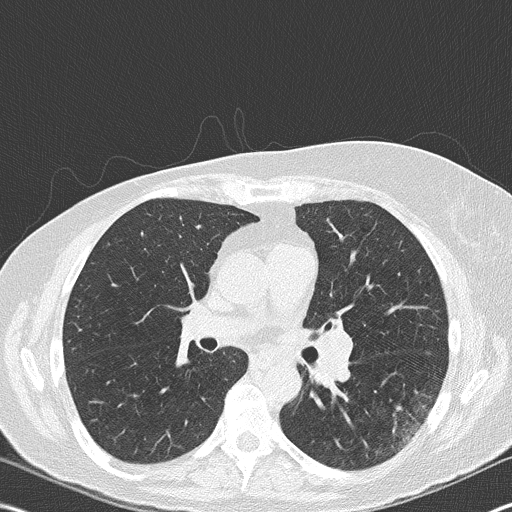
Low-dose screening chest CT, one axial slice; slice 101 of 177 in the series (ordered by position); reconstruction kernel B50f; lung window (W 1500 / L -600 HU); 512 × 512 image matrix, field of view 342 × 342 mm.
Structures marked on this image (manually delineated by an expert):
- lesion 2 (nodule, hilum of left lung): bounding box <317,331,354,385> (left, top, right, bottom; pixels)